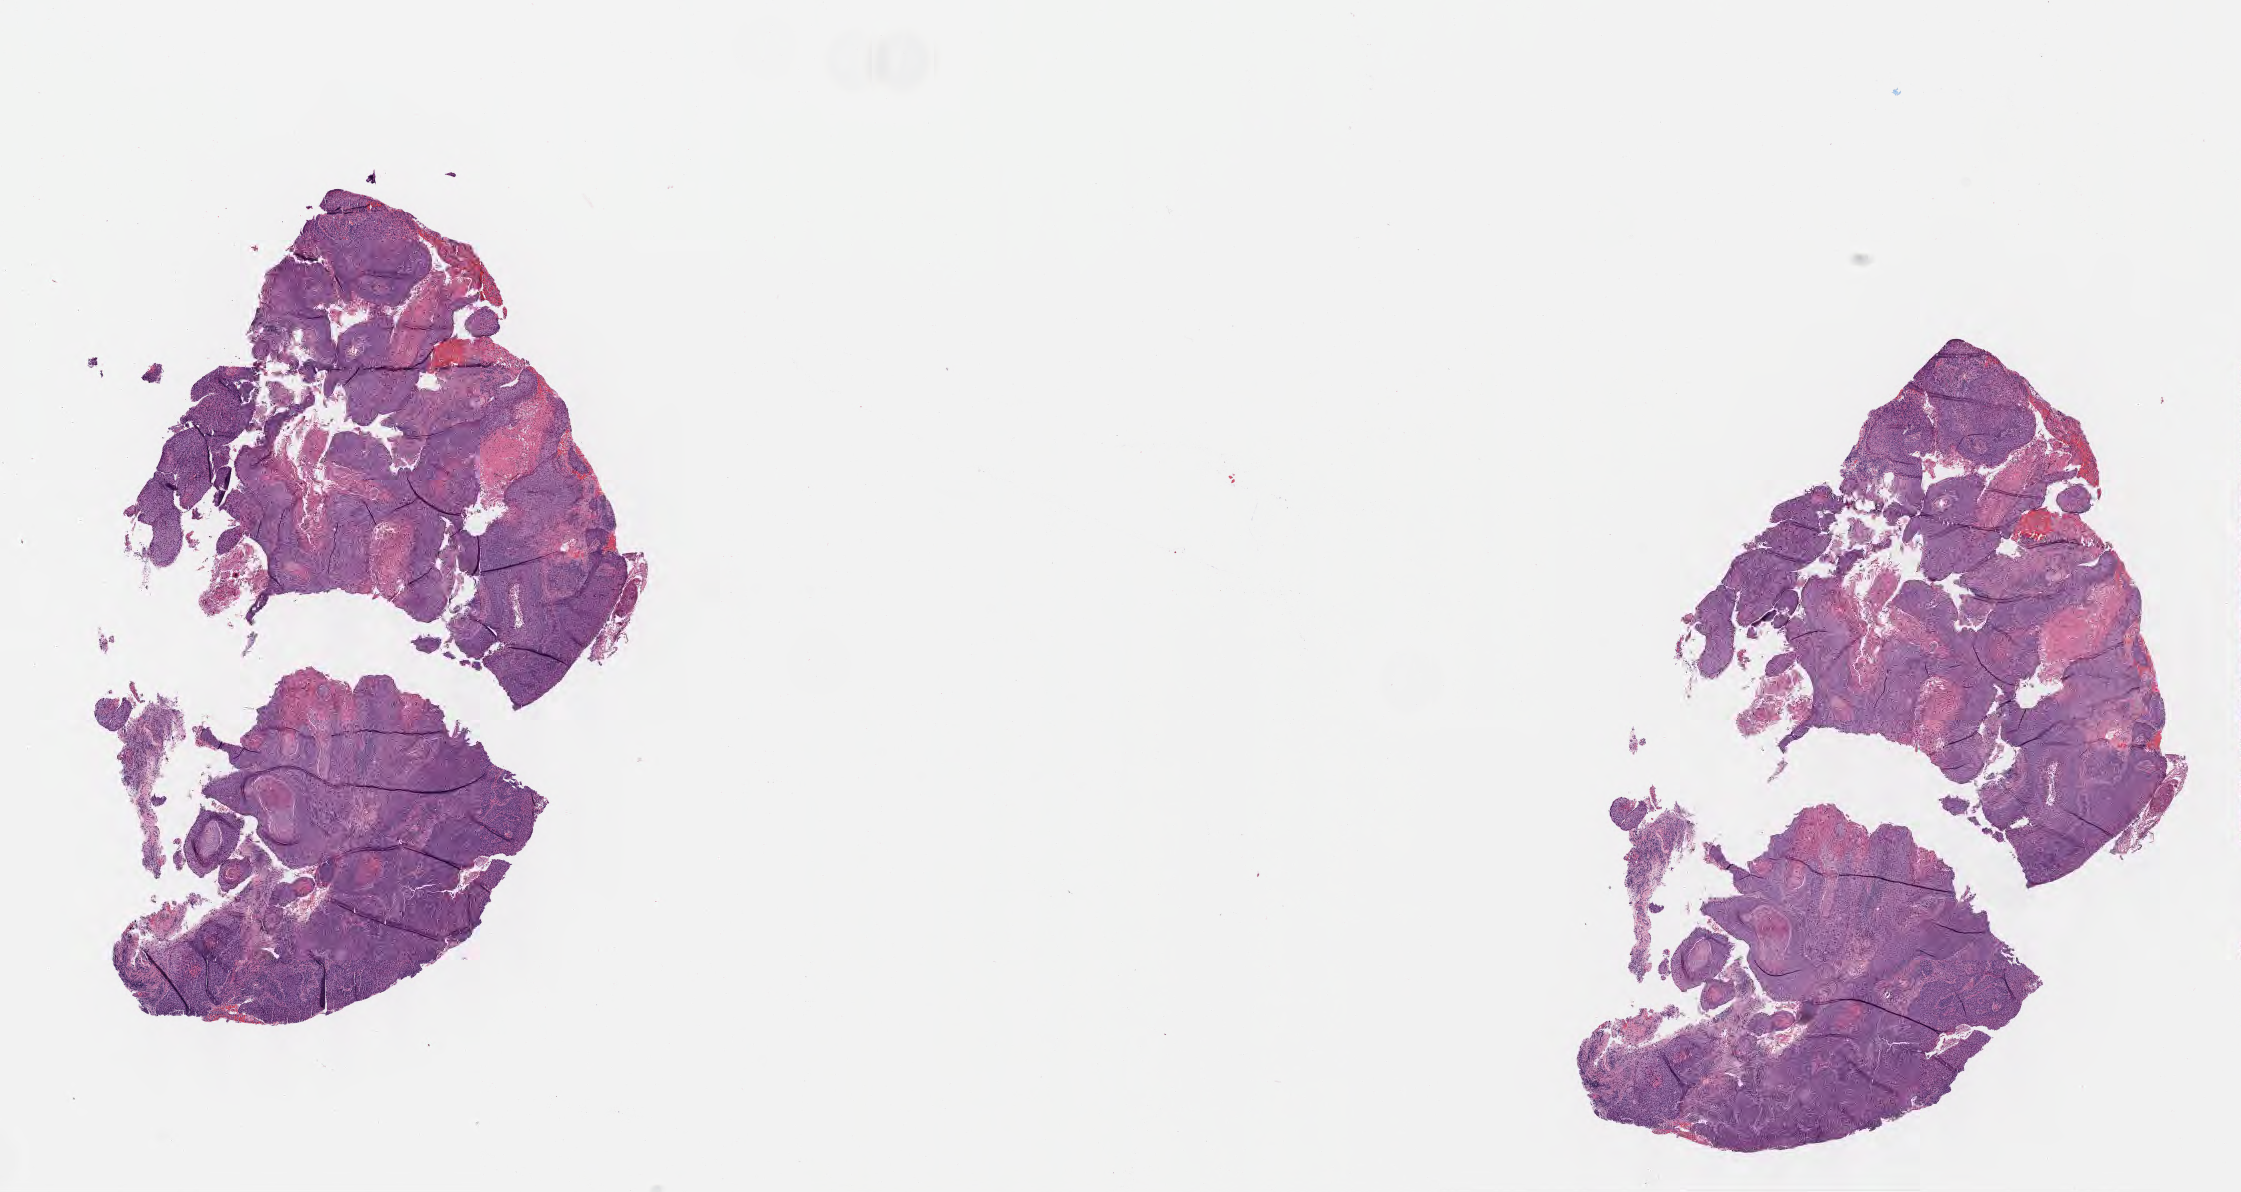
Whole-slide image, hematoxylin and eosin (H&E) stain — shown as a low-resolution overview of the whole scanned area (about 18.1 x 9.6 mm); tumor tissue; anatomic site: cervix. Patient: female, age 32 years.
* histologic diagnosis: Squamous cell carcinoma, keratinizing, NOS